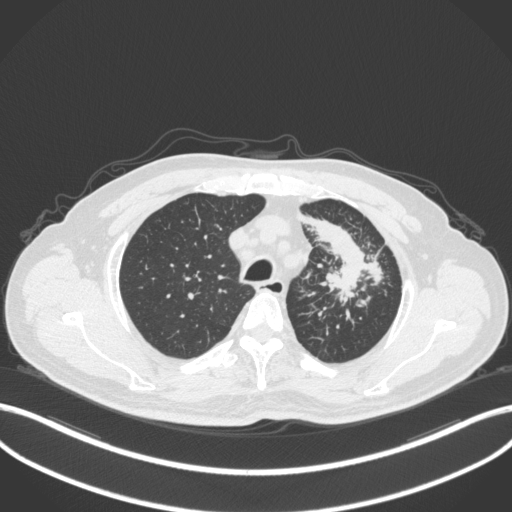
Chest CT, one axial slice; lung window (W 1500 / L -600 HU); 1 mm slice thickness; 512 × 512 image matrix, field of view 400 × 400 mm. Patient: male, 69 years. From the clinical record (not read from this slice): clinical TNM (as recorded): T2a N2 M0.
Structures marked on this image (bounding box drawn by a radiologist):
- lung tumour (recorded histology: adenocarcinoma): bounding box <301,206,389,302> (left, top, right, bottom; pixels)